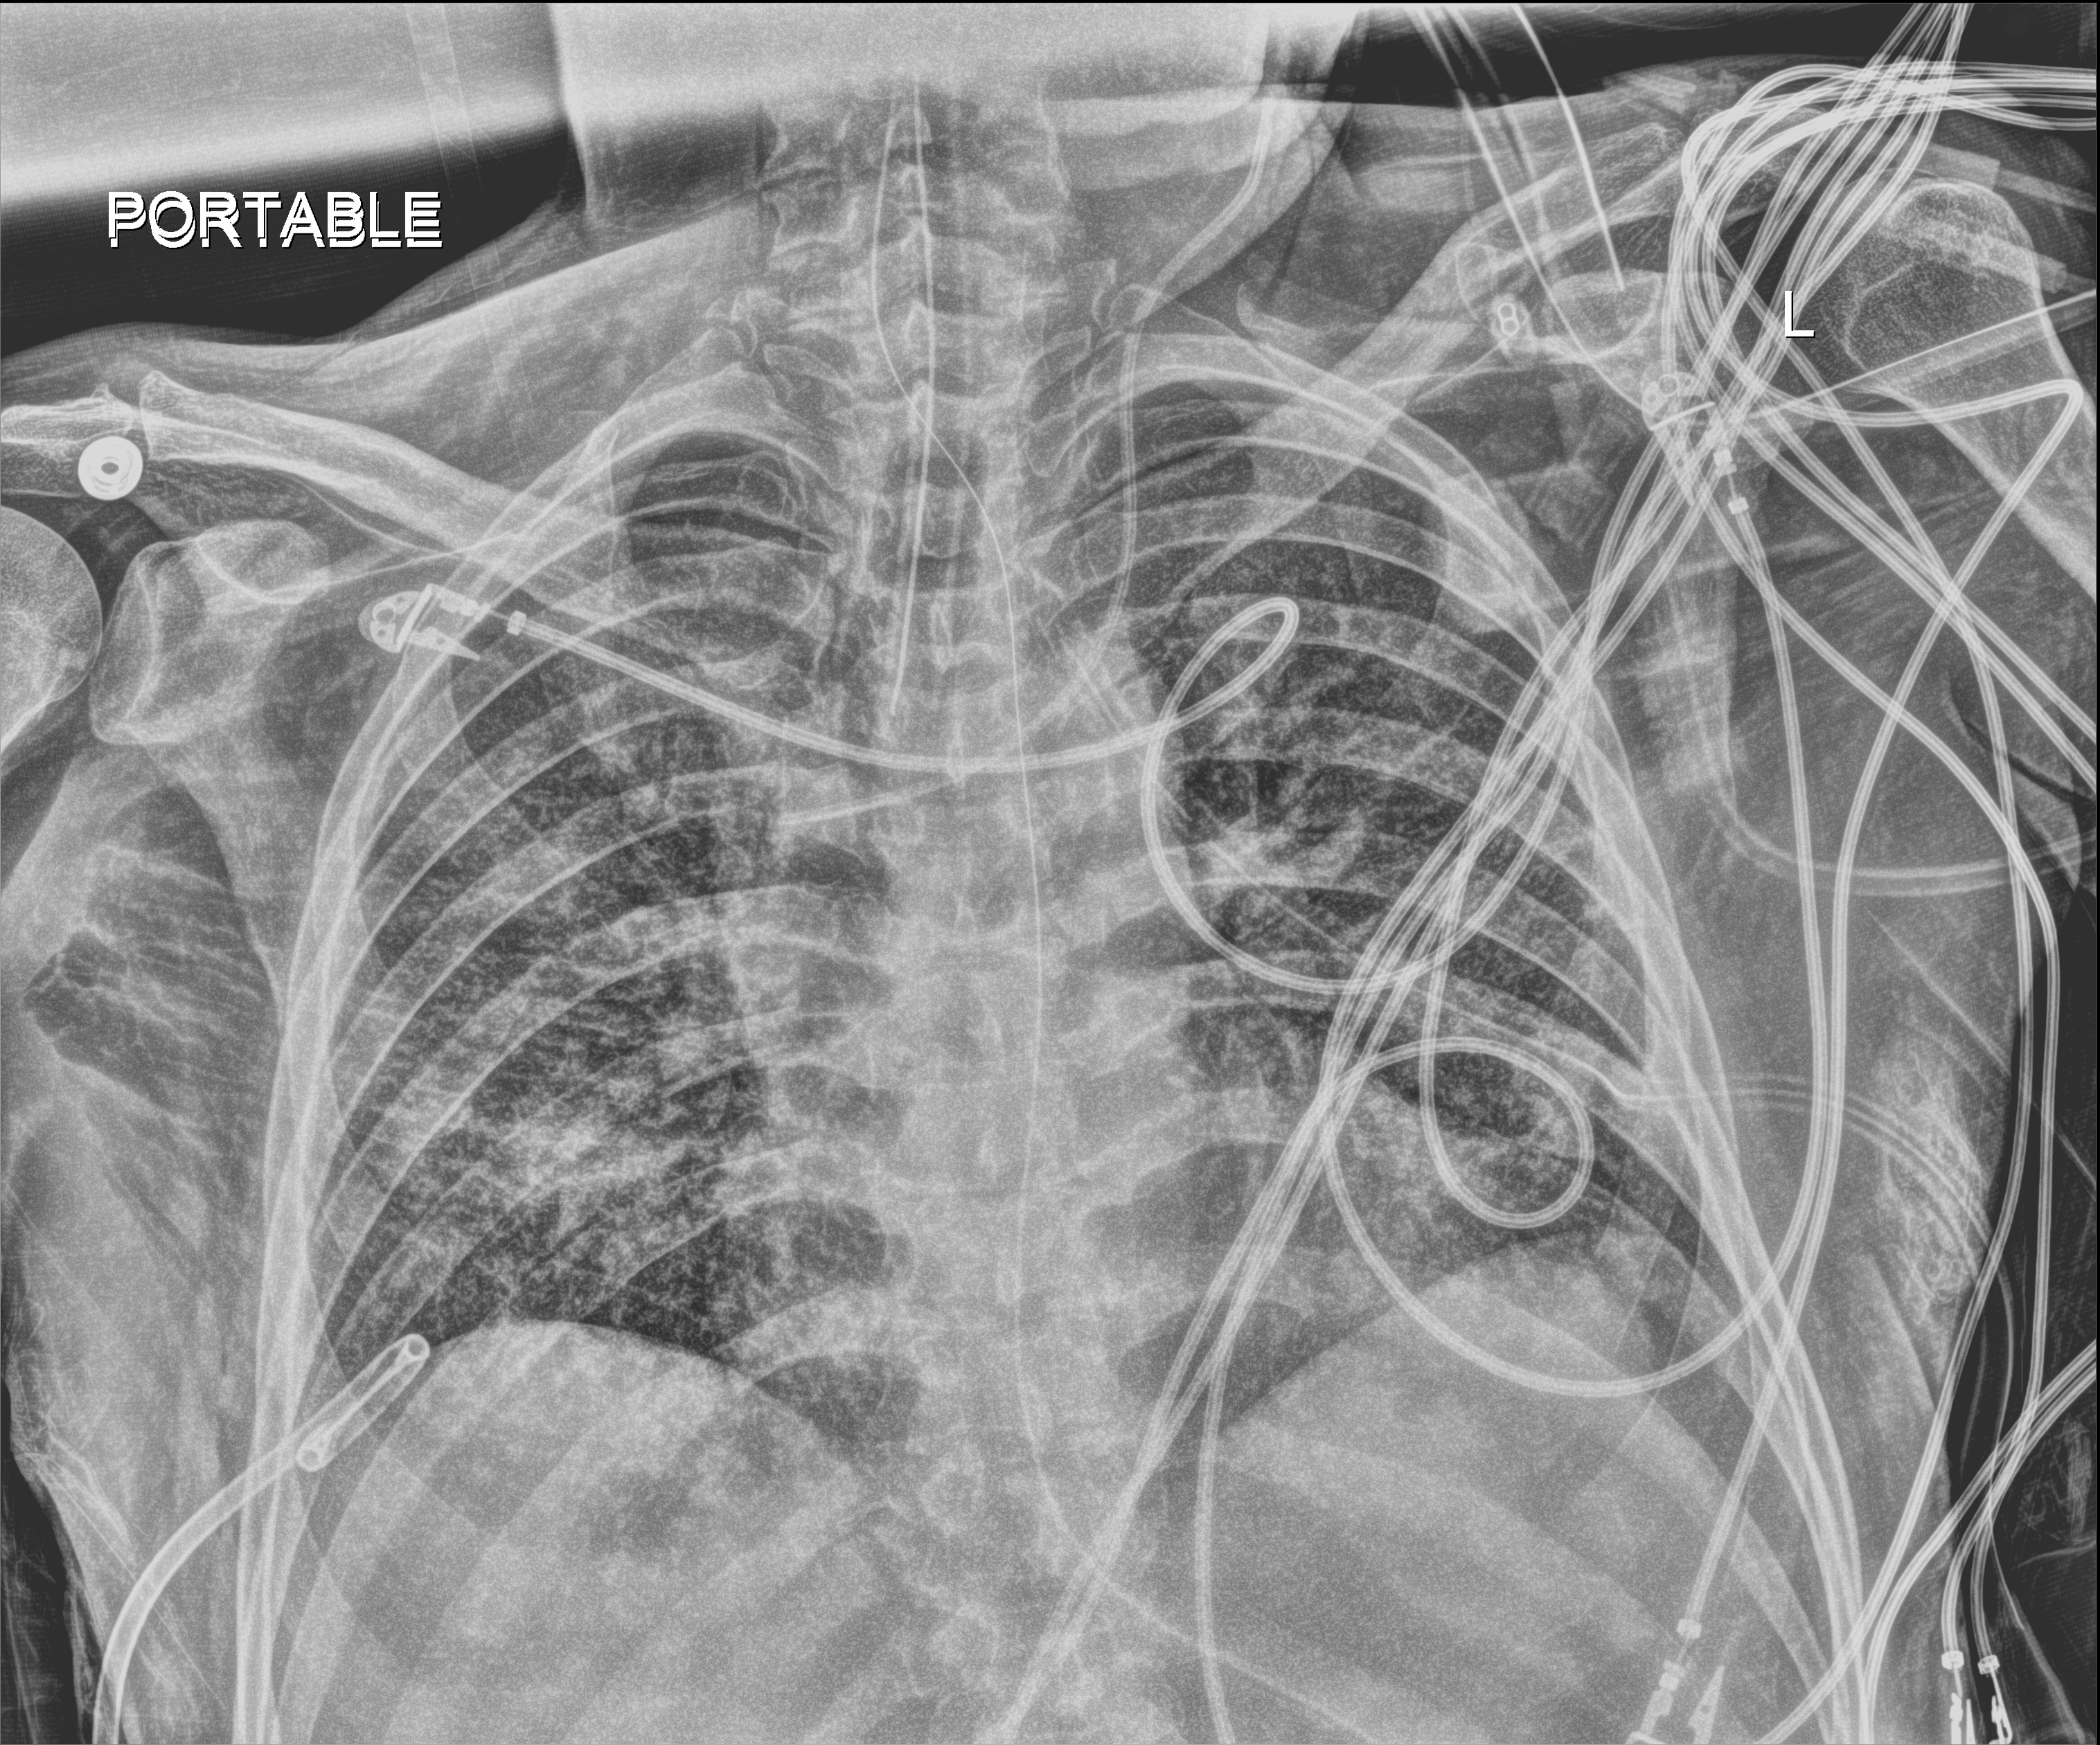
Chest radiograph; anteroposterior (AP) projection. Patient hospitalised with COVID-19; male, aged 18–59 years.
Admission-level facts for this patient (not findings on this image; timing relative to this image not recorded): mechanically ventilated during this hospital stay: yes.